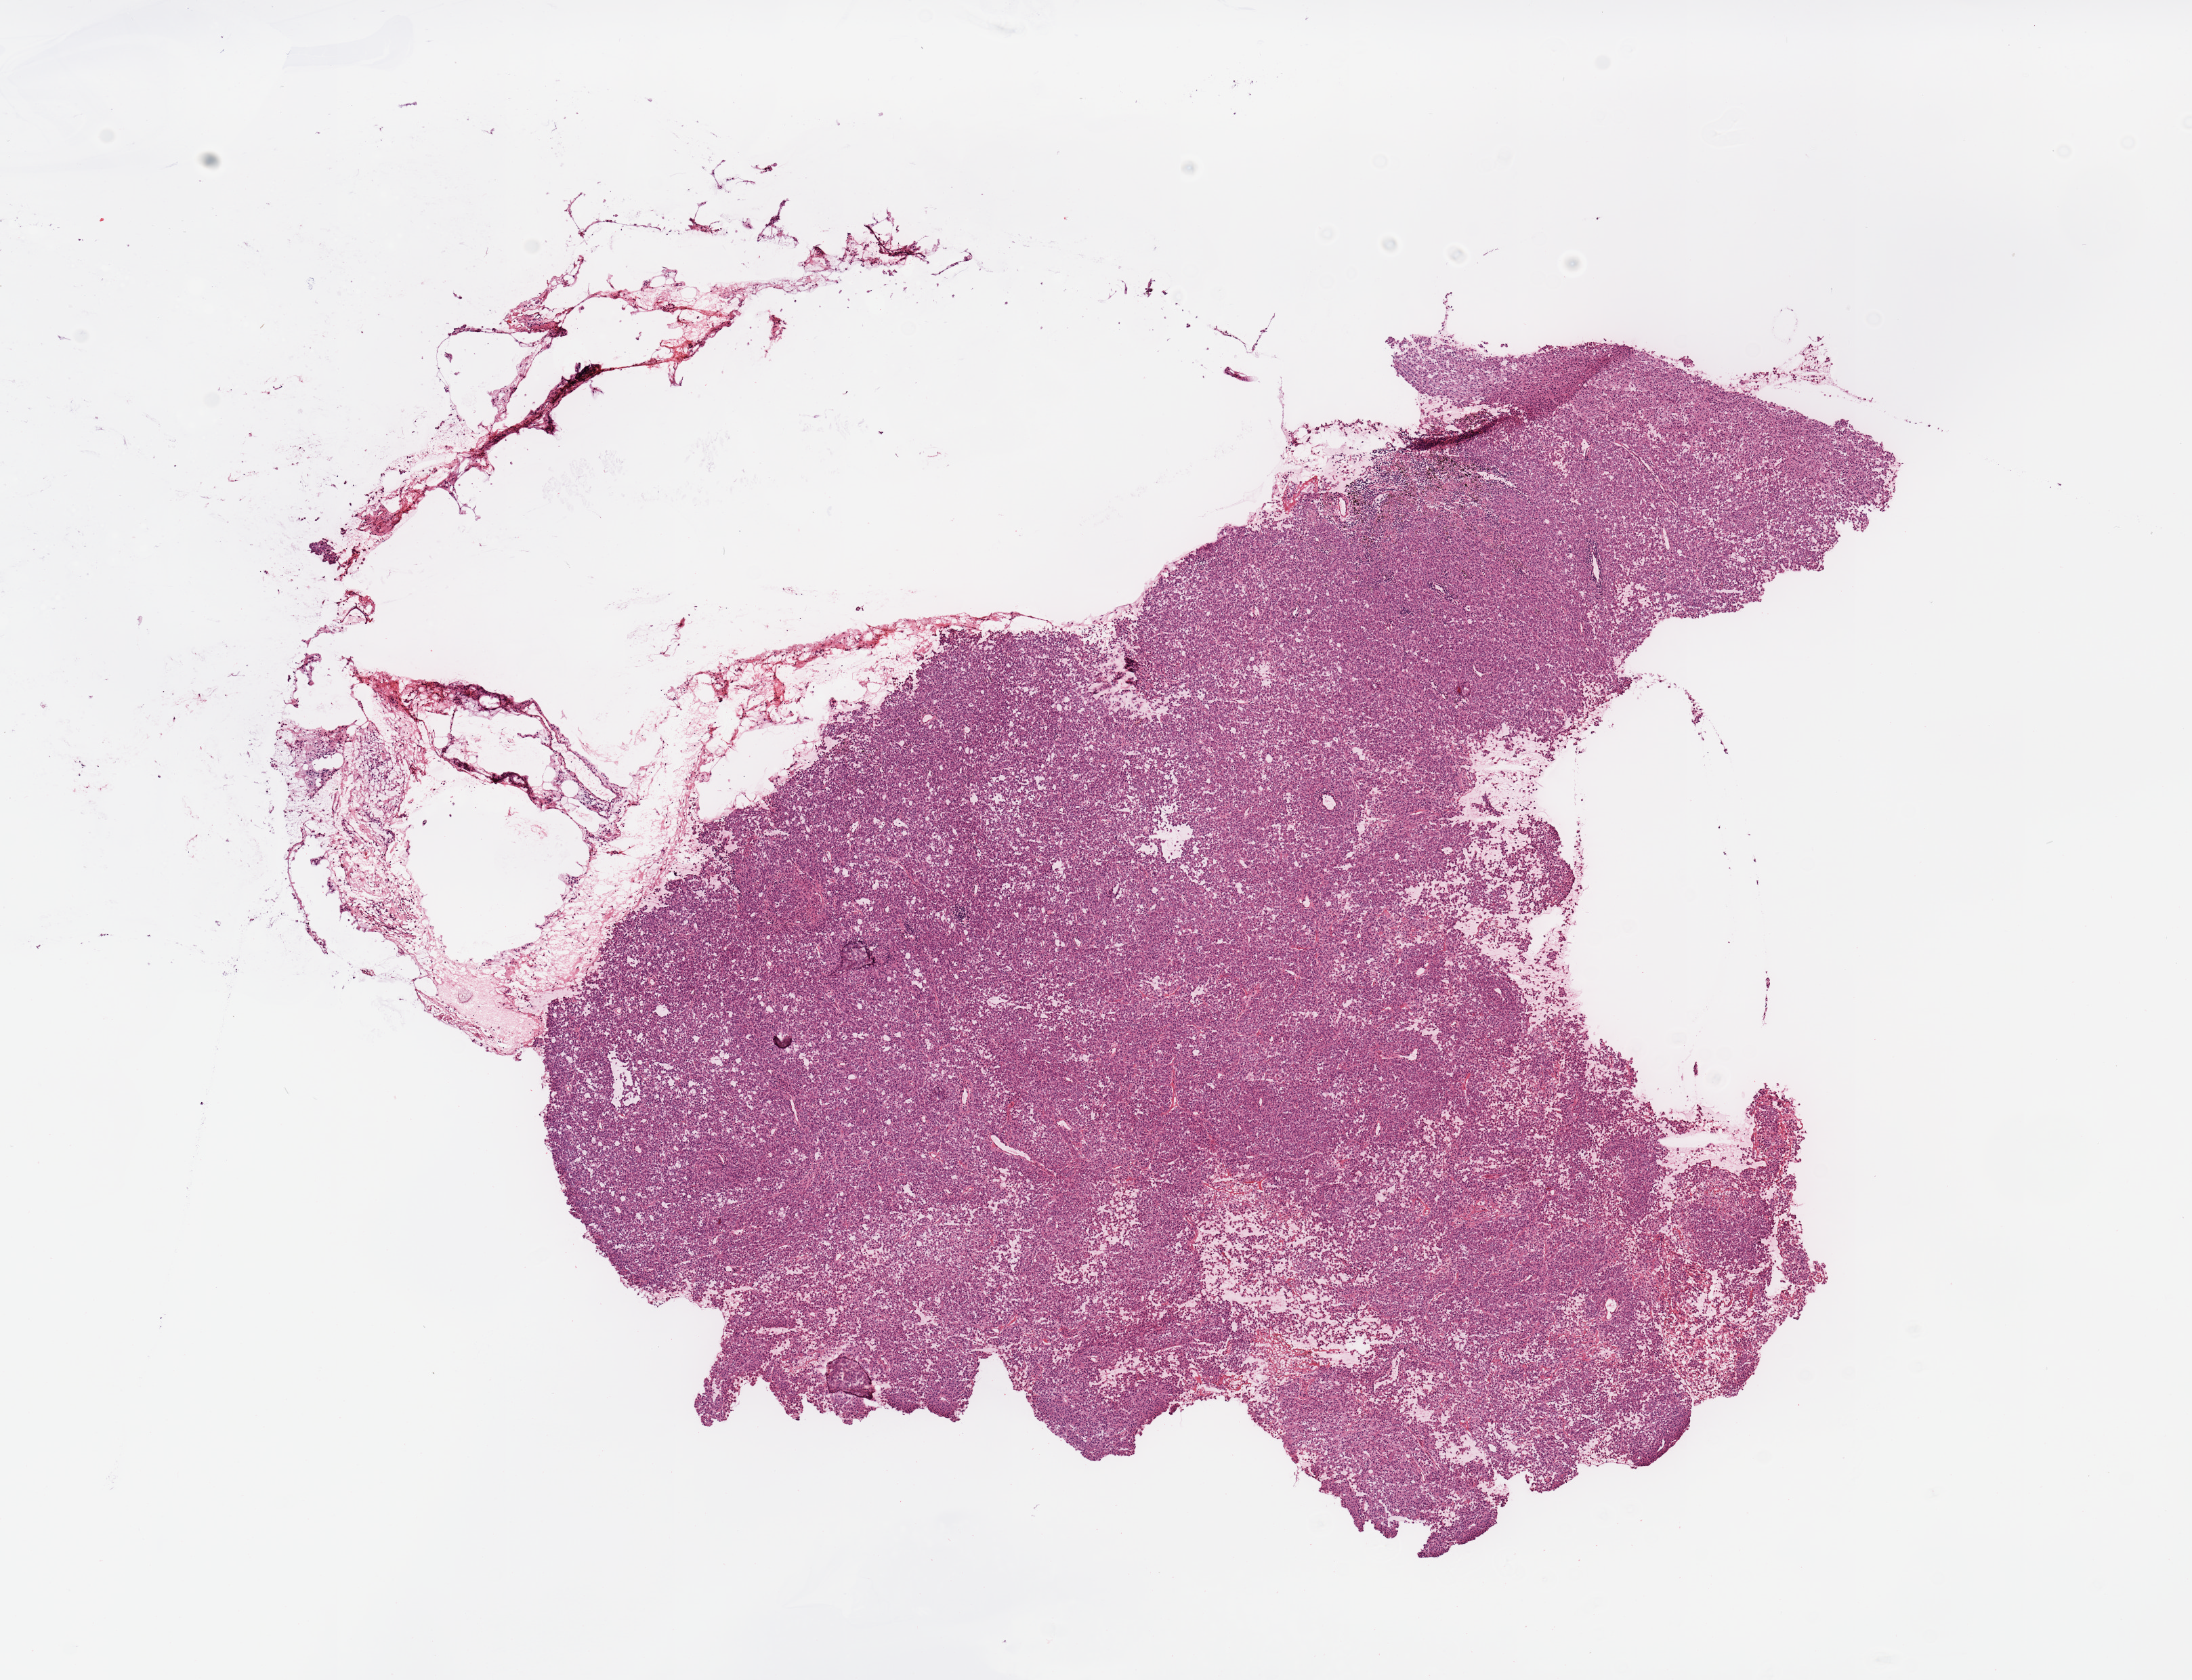
H&E whole-slide image, a low-resolution overview of the entire scanned area, about 12.8 x 9.8 mm (acquisition: 20x scan), melanoma tumour tissue; sampled site not recorded. Male, 51 y/o.
Patient diagnosis (cohort enrolment): cutaneous melanoma (skin).